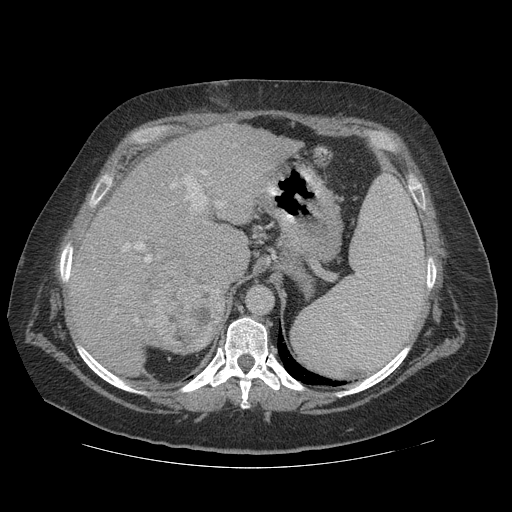
Contrast-enhanced abdominal CT (liver protocol), one axial slice. Position 83 of 121 along the scan axis. Reconstruction kernel STANDARD. 140 kVp. Soft-tissue window (W 400 / L 40 HU). 512 × 512 image matrix. Case-level facts recorded for this patient, not image findings: diagnosis: hepatocellular carcinoma (patient treated with transarterial chemoembolisation; whether this scan precedes or follows treatment is not stated here); TNM stage (as recorded): Stage-IIIA; Child-Pugh class: A; tumour nodularity: multinodular; tumour size: 7.4 cm.
Outlined on this slice (semi-automatic segmentation, software-assisted and operator-edited):
- liver parenchyma outside the tumour (the mass and vessels are separate outlines, so this box may not span the whole liver): bounding box <68,122,301,368> (left, top, right, bottom; pixels)
- mass: <133,253,226,354>
- liver vessels: <82,145,257,320>